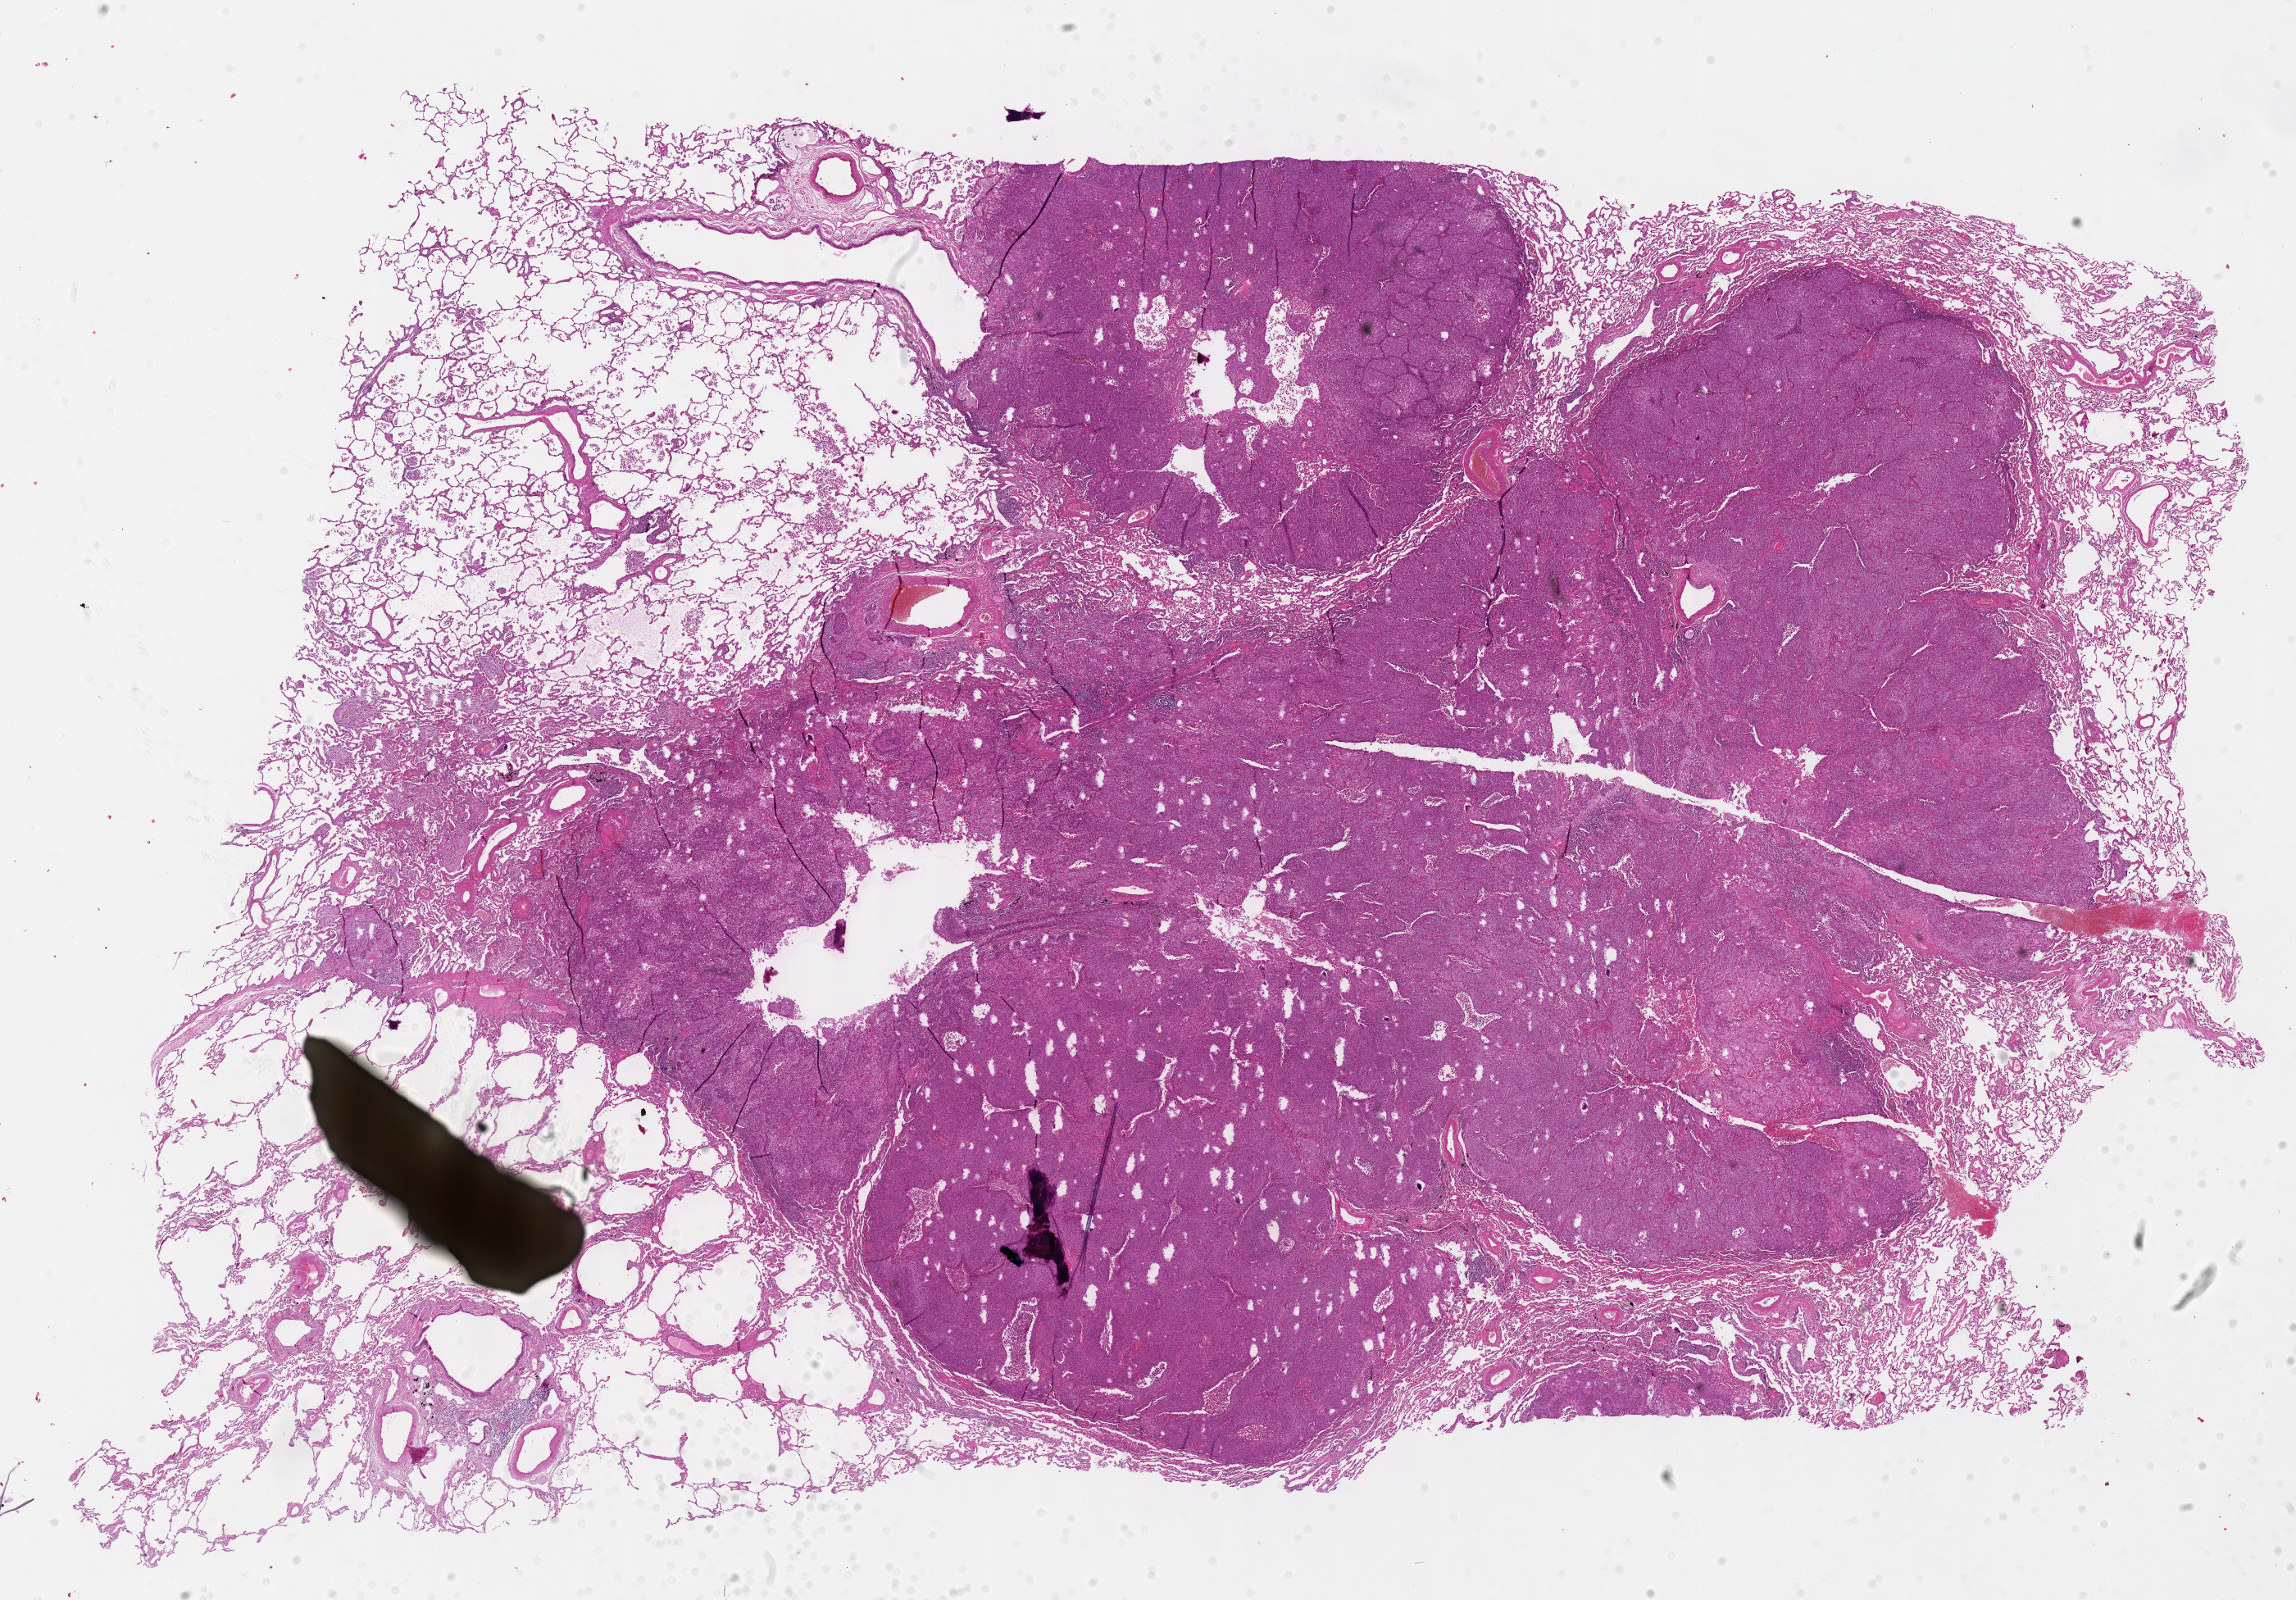
H&E-stained whole-slide image, low-resolution overview of the scanned area, about 22.6 x 15.8 mm, FFPE section, lung, primary tumour sample. Male patient; age at initial diagnosis 69 years.
* TNM: T2a N0 M1b
* AJCC pathologic stage: IV
* diagnosis: Squamous cell carcinoma, keratinizing, NOS (upper lobe, lung)
* laterality: left